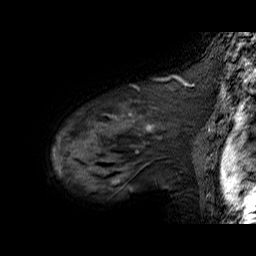
Breast MRI (dynamic contrast-enhanced), one sagittal slice; slice 52 of 60 in the series (ordered by position); dynamic contrast-enhanced series, time point 2 of 6 at this slice position (early post-contrast); 1.5 T; TE 6.3 ms, TR 32.9 ms; 4 mm slice thickness; 256 × 256 image matrix. Female patient. Case-level facts recorded for this patient, not image findings: setting: breast cancer imaged before/during neoadjuvant chemotherapy; receptor status: HER2-positive.
Outlined on this slice (semi-automatic segmentation, software-assisted and operator-edited):
- analysis volume of interest (the breast-tissue region the enhancement analysis was run in; not a lesion): bounding box <53,92,195,174> (left, top, right, bottom; pixels)
- tumour enhancement mask (voxels above the 100 % enhancement threshold inside the analysis volume of interest): <53,114,154,172>